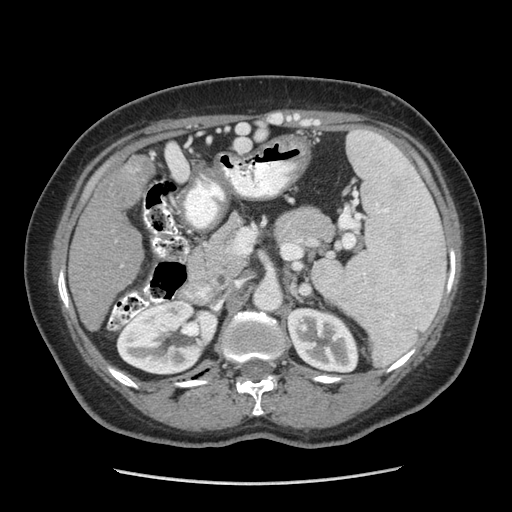
Contrast-enhanced abdominal CT (liver protocol), one axial slice; reconstruction kernel STANDARD; 140 kVp; soft-tissue window (W 400 / L 40 HU); 2.5 mm slice thickness; 512 × 512 image matrix, field of view 360 × 360 mm. Case-level facts recorded for this patient, not image findings: diagnosis: hepatocellular carcinoma (patient treated with transarterial chemoembolisation; whether this scan precedes or follows treatment is not stated here); TNM stage (as recorded): Stage-I; Child-Pugh class: A; tumour differentiation: poorly differentiated; tumour nodularity: uninodular.
Annotated regions visible in this slice (semi-automatically segmented with operator editing):
- liver parenchyma outside the tumour (the mass and vessels are separate outlines, so this box may not span the whole liver): box from (x=68, y=151) to (x=156, y=330) px
- mass: (x=91, y=158)–(x=152, y=216)
- liver vessels: (x=152, y=153)–(x=154, y=155)